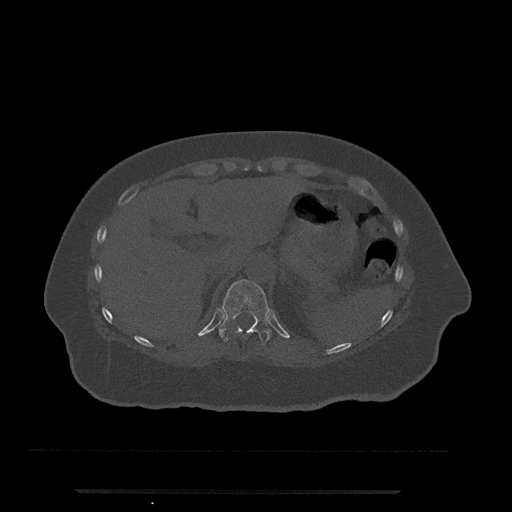
CT including the spine, one axial slice; position 238 of 797 along the scan axis; bone window (W 1800 / L 400 HU); 0.5 mm slice thickness; 512 × 512 image matrix, field of view 440 × 440 mm. Female patient, age 51 years. From the clinical record (not read from this slice): primary cancer: neuro.
Outlined on this slice (semi-automatically segmented with operator editing):
- T11 vertebra: bounding box <219,279,271,346> (left, top, right, bottom; pixels)